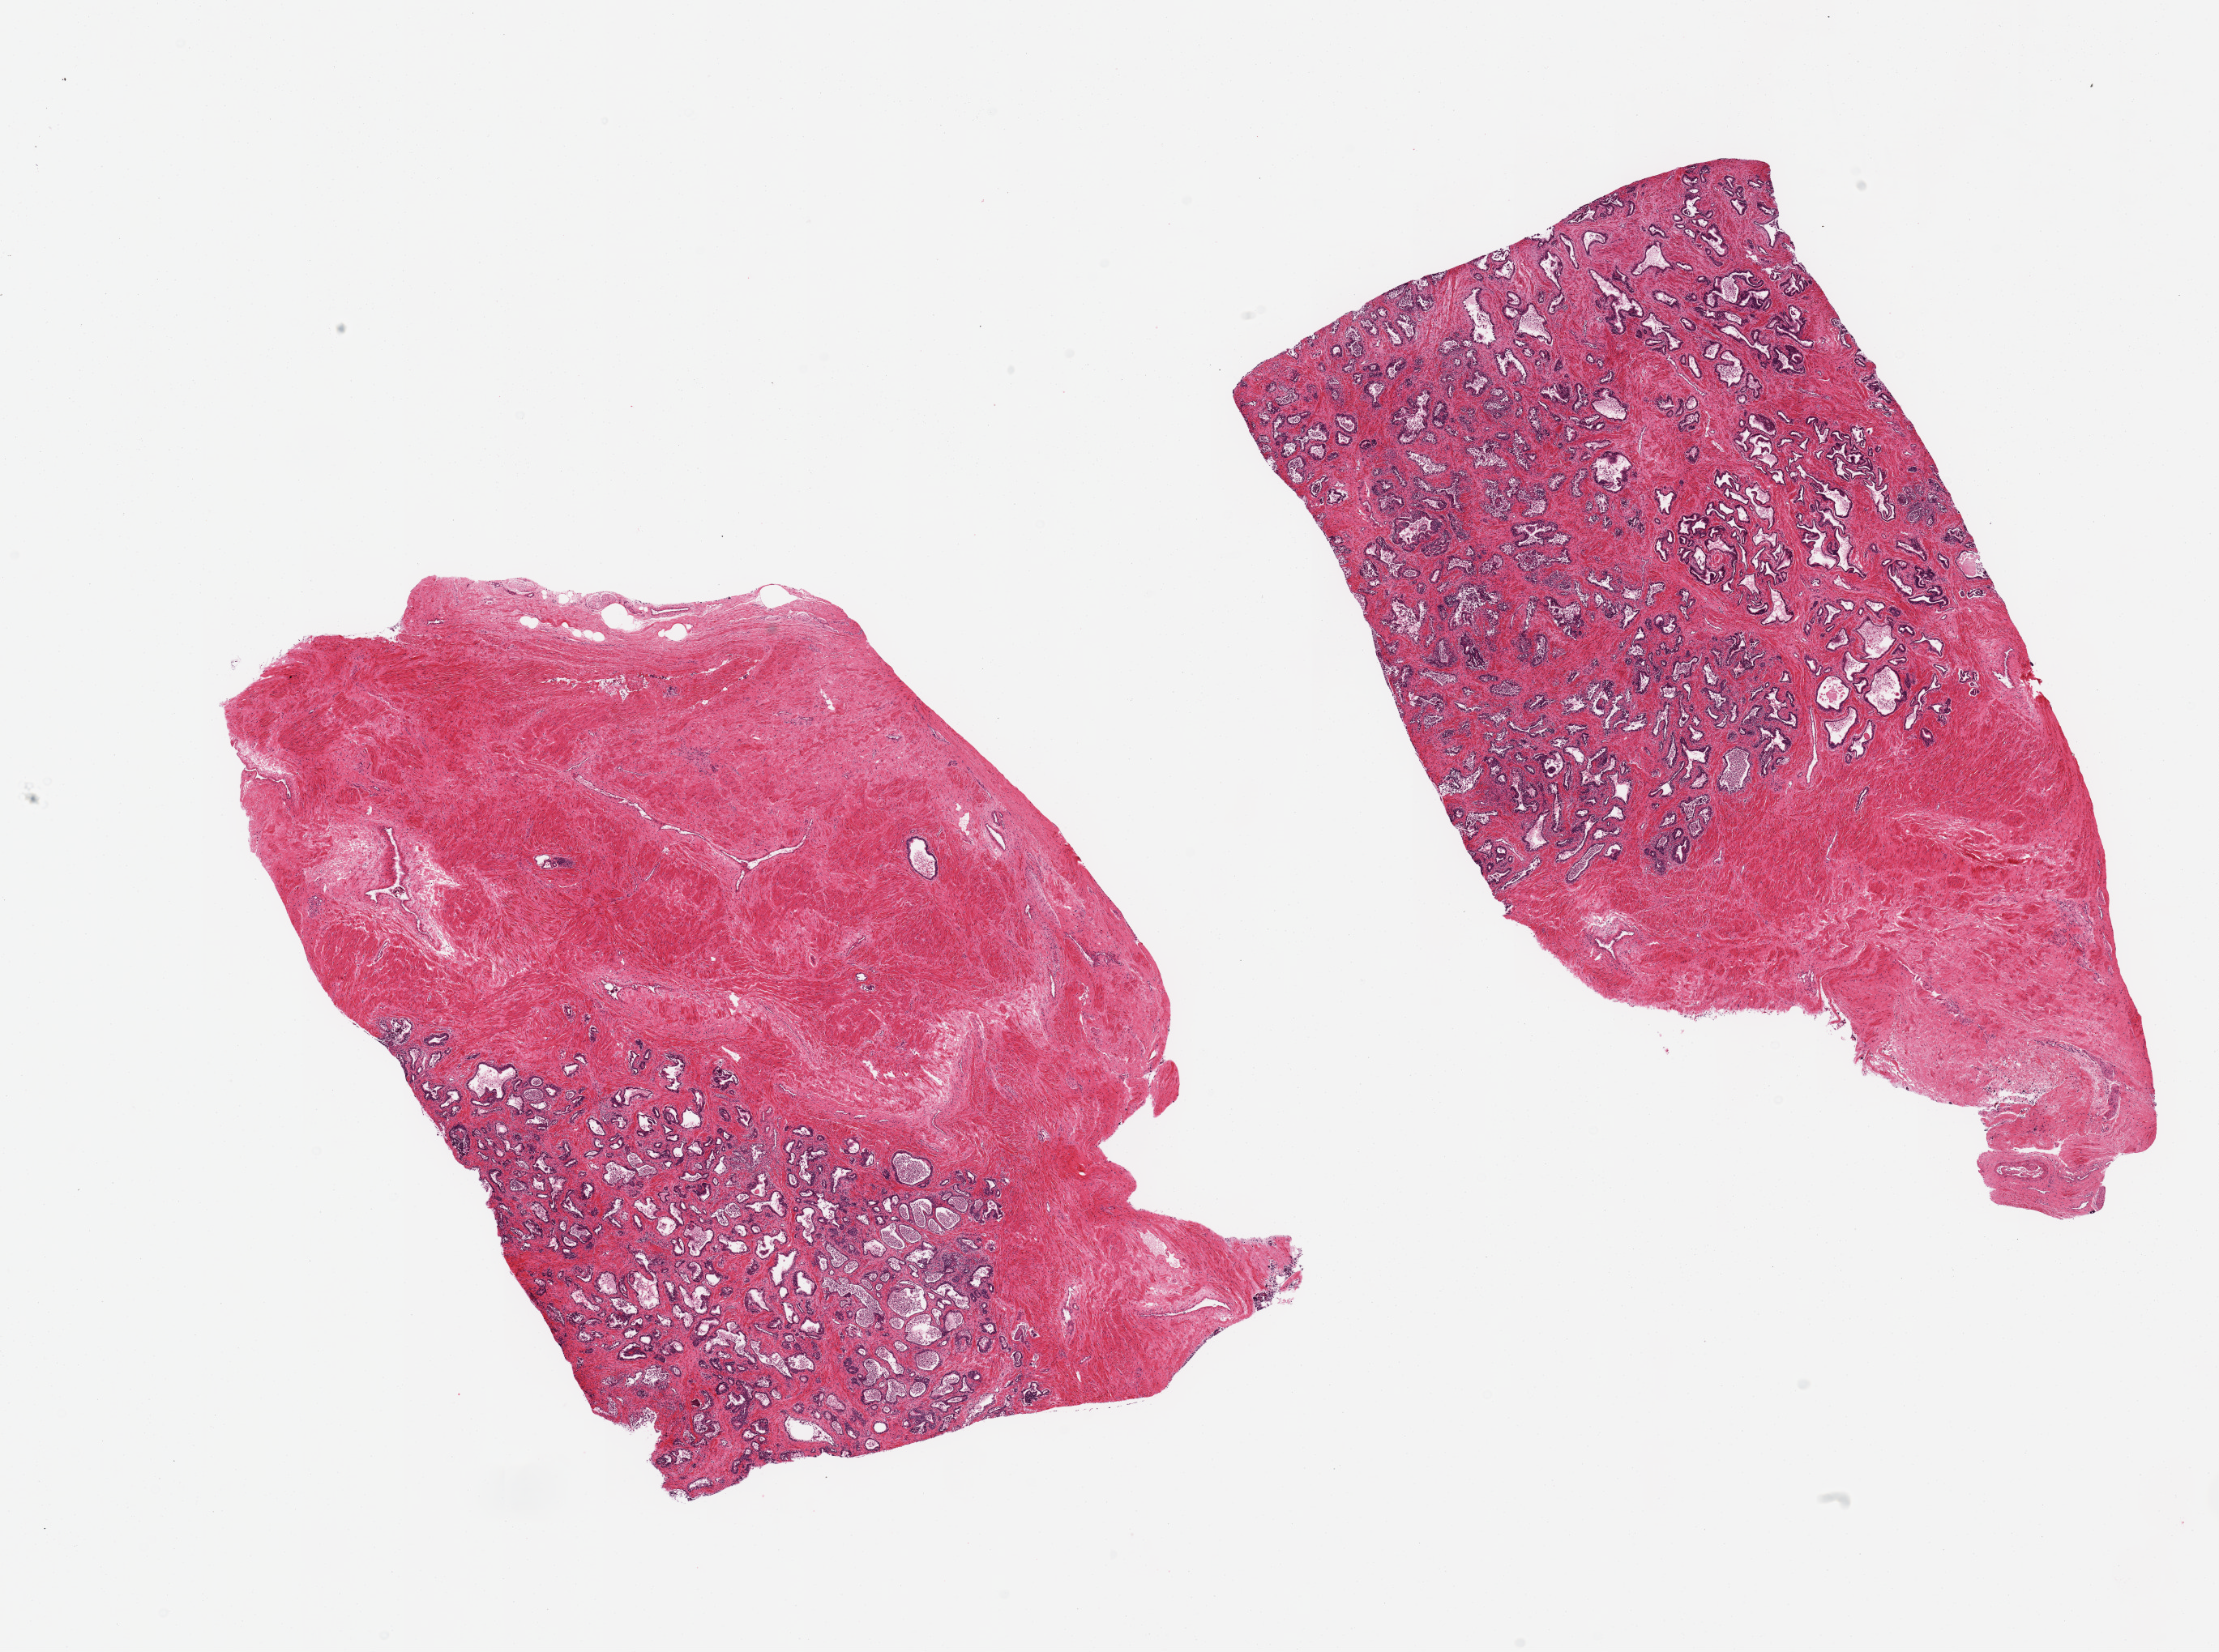
Whole-slide image, hematoxylin and eosin (H&E) stain, brightfield — a low-resolution overview of the entire scanned area, about 21.7 x 16.1 mm. PAXgene-fixed paraffin-embedded (PFPE) section. Target tissue: prostate. Tissue donor sample. Male donor.
- reviewer comment on this tissue sample: 2 pieces, acute prostatitis